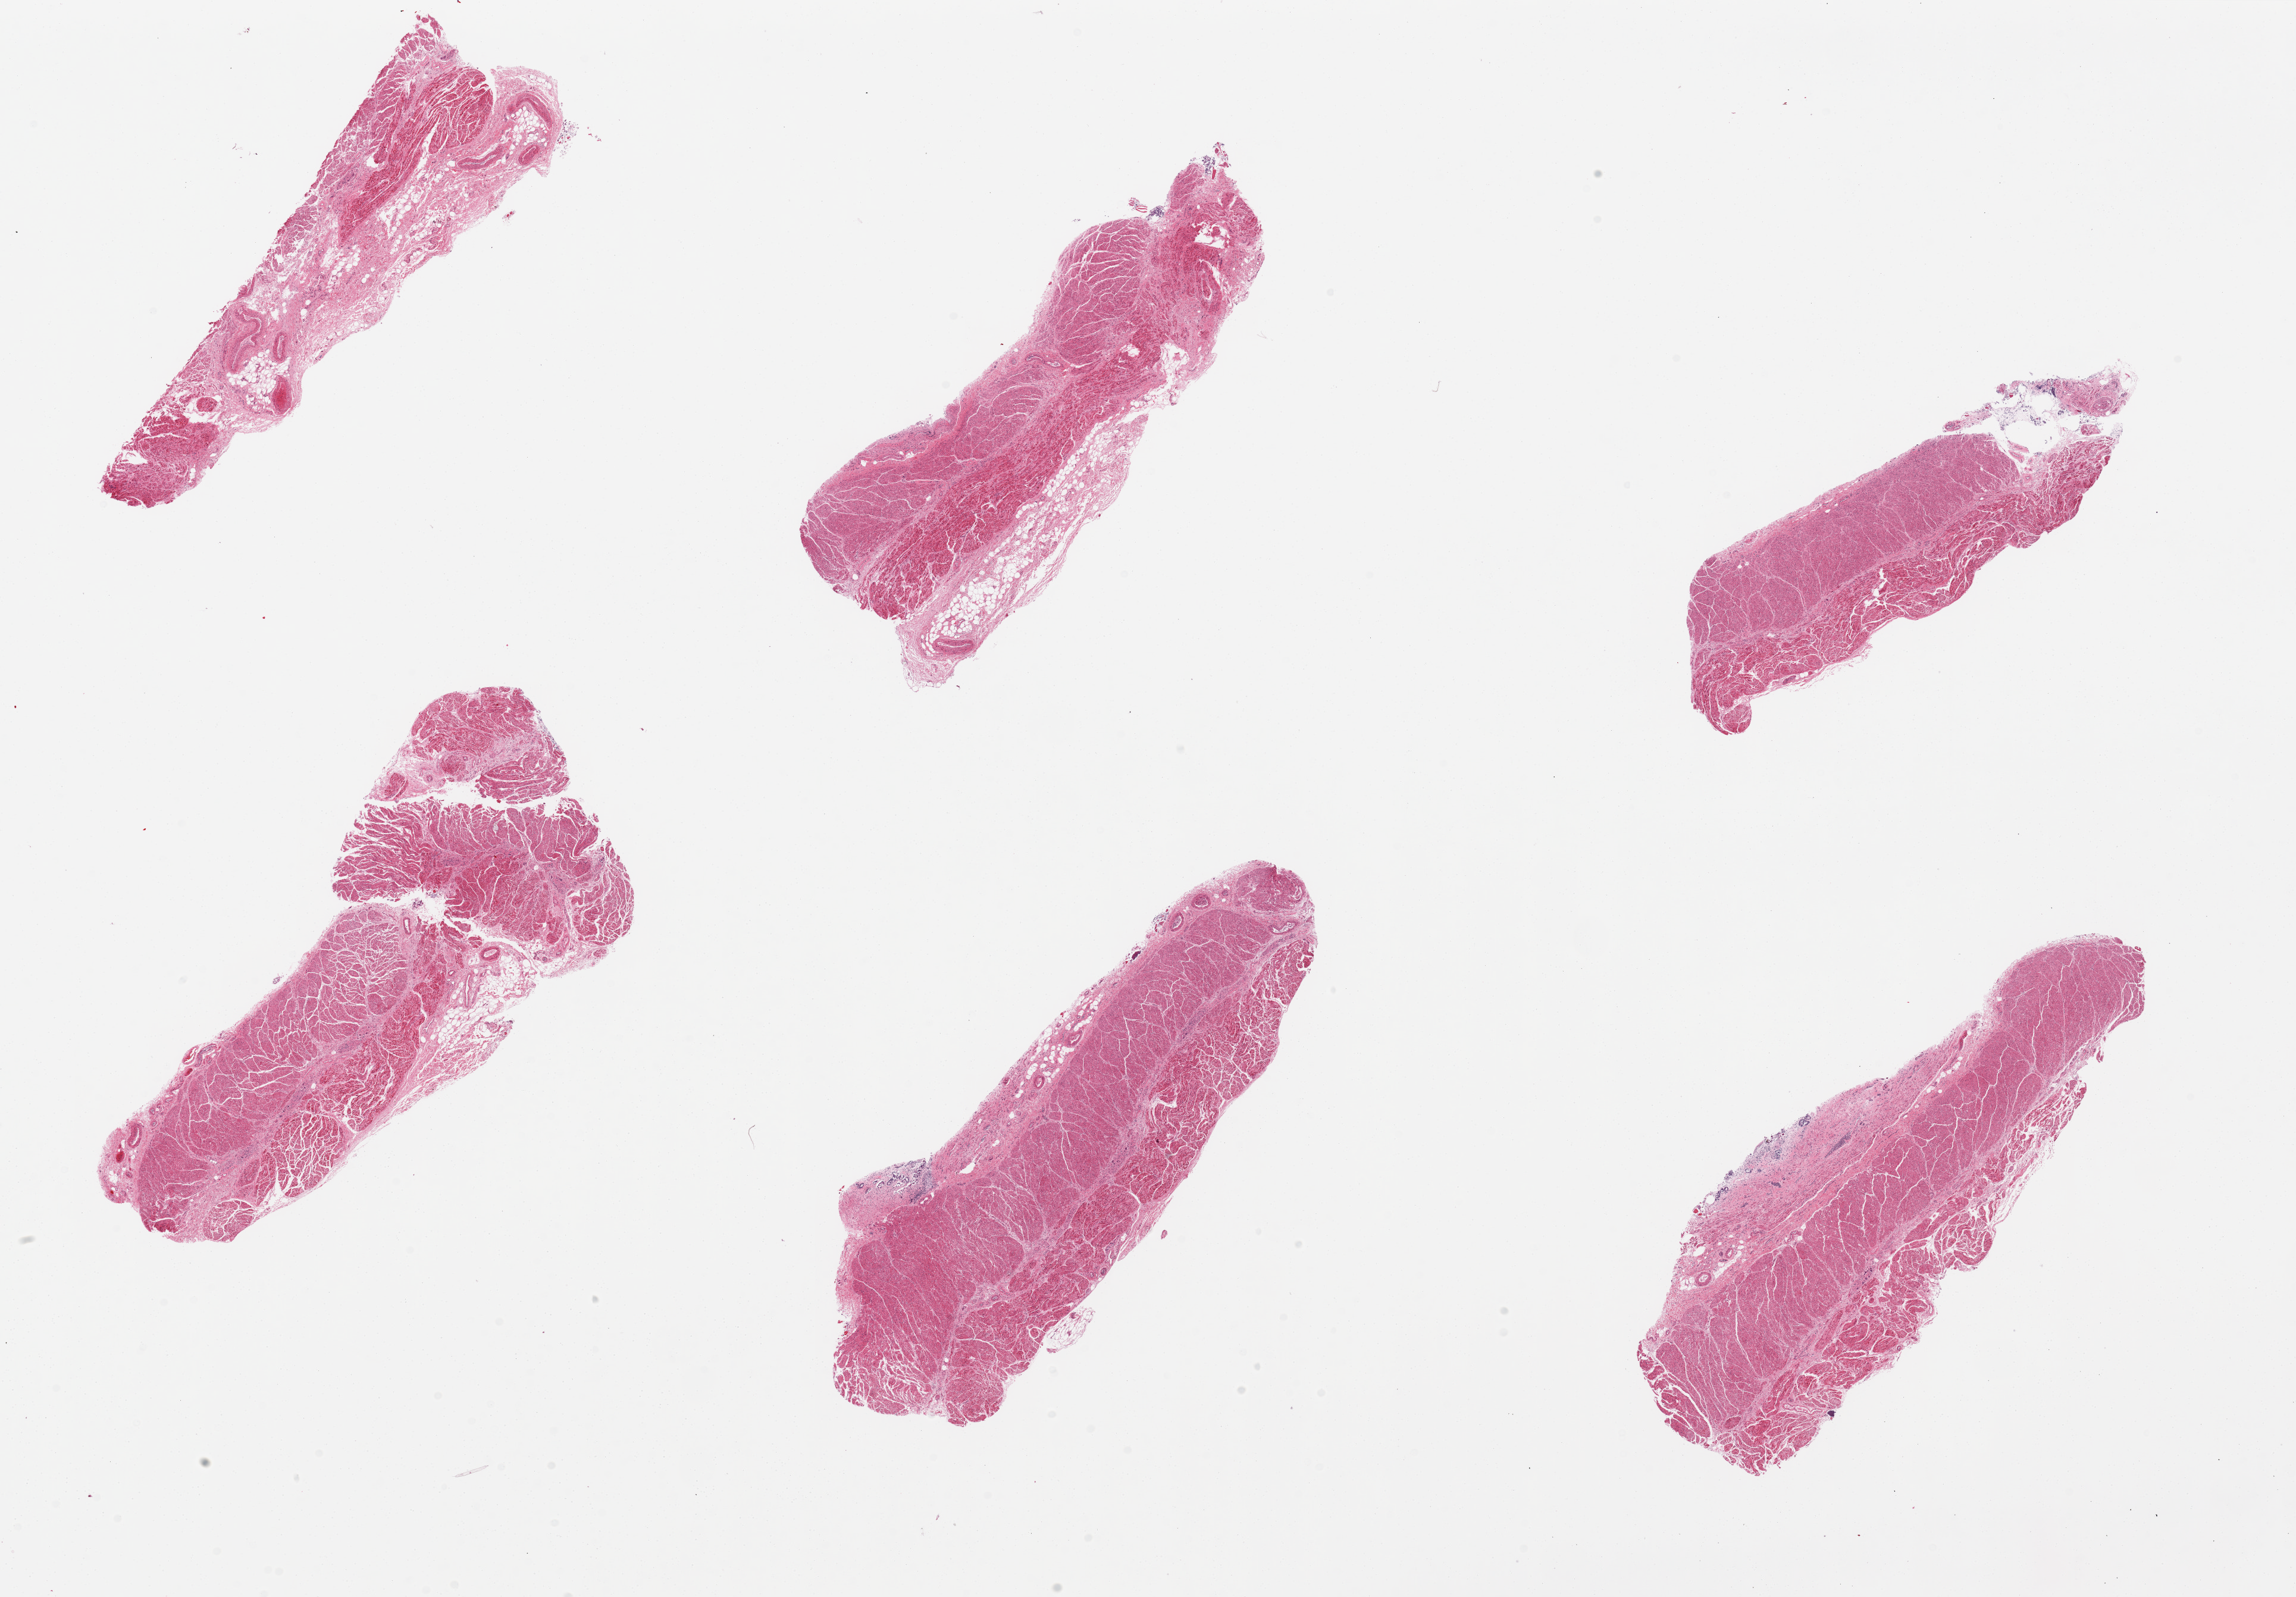
Whole-slide image, hematoxylin and eosin (H&E) stain, brightfield — whole scanned area (about 30.5 x 21.2 mm, acquisition: 20x scan) shown as a low-resolution overview; PAXgene-fixed paraffin-embedded (PFPE) section; sampled site (target tissue): gastroesophageal junction; donor tissue sample.
Review note (as recorded): 6 pieces: 1 has 70% fibrofatty tissue; 1 has 1 mm thick submucosa.